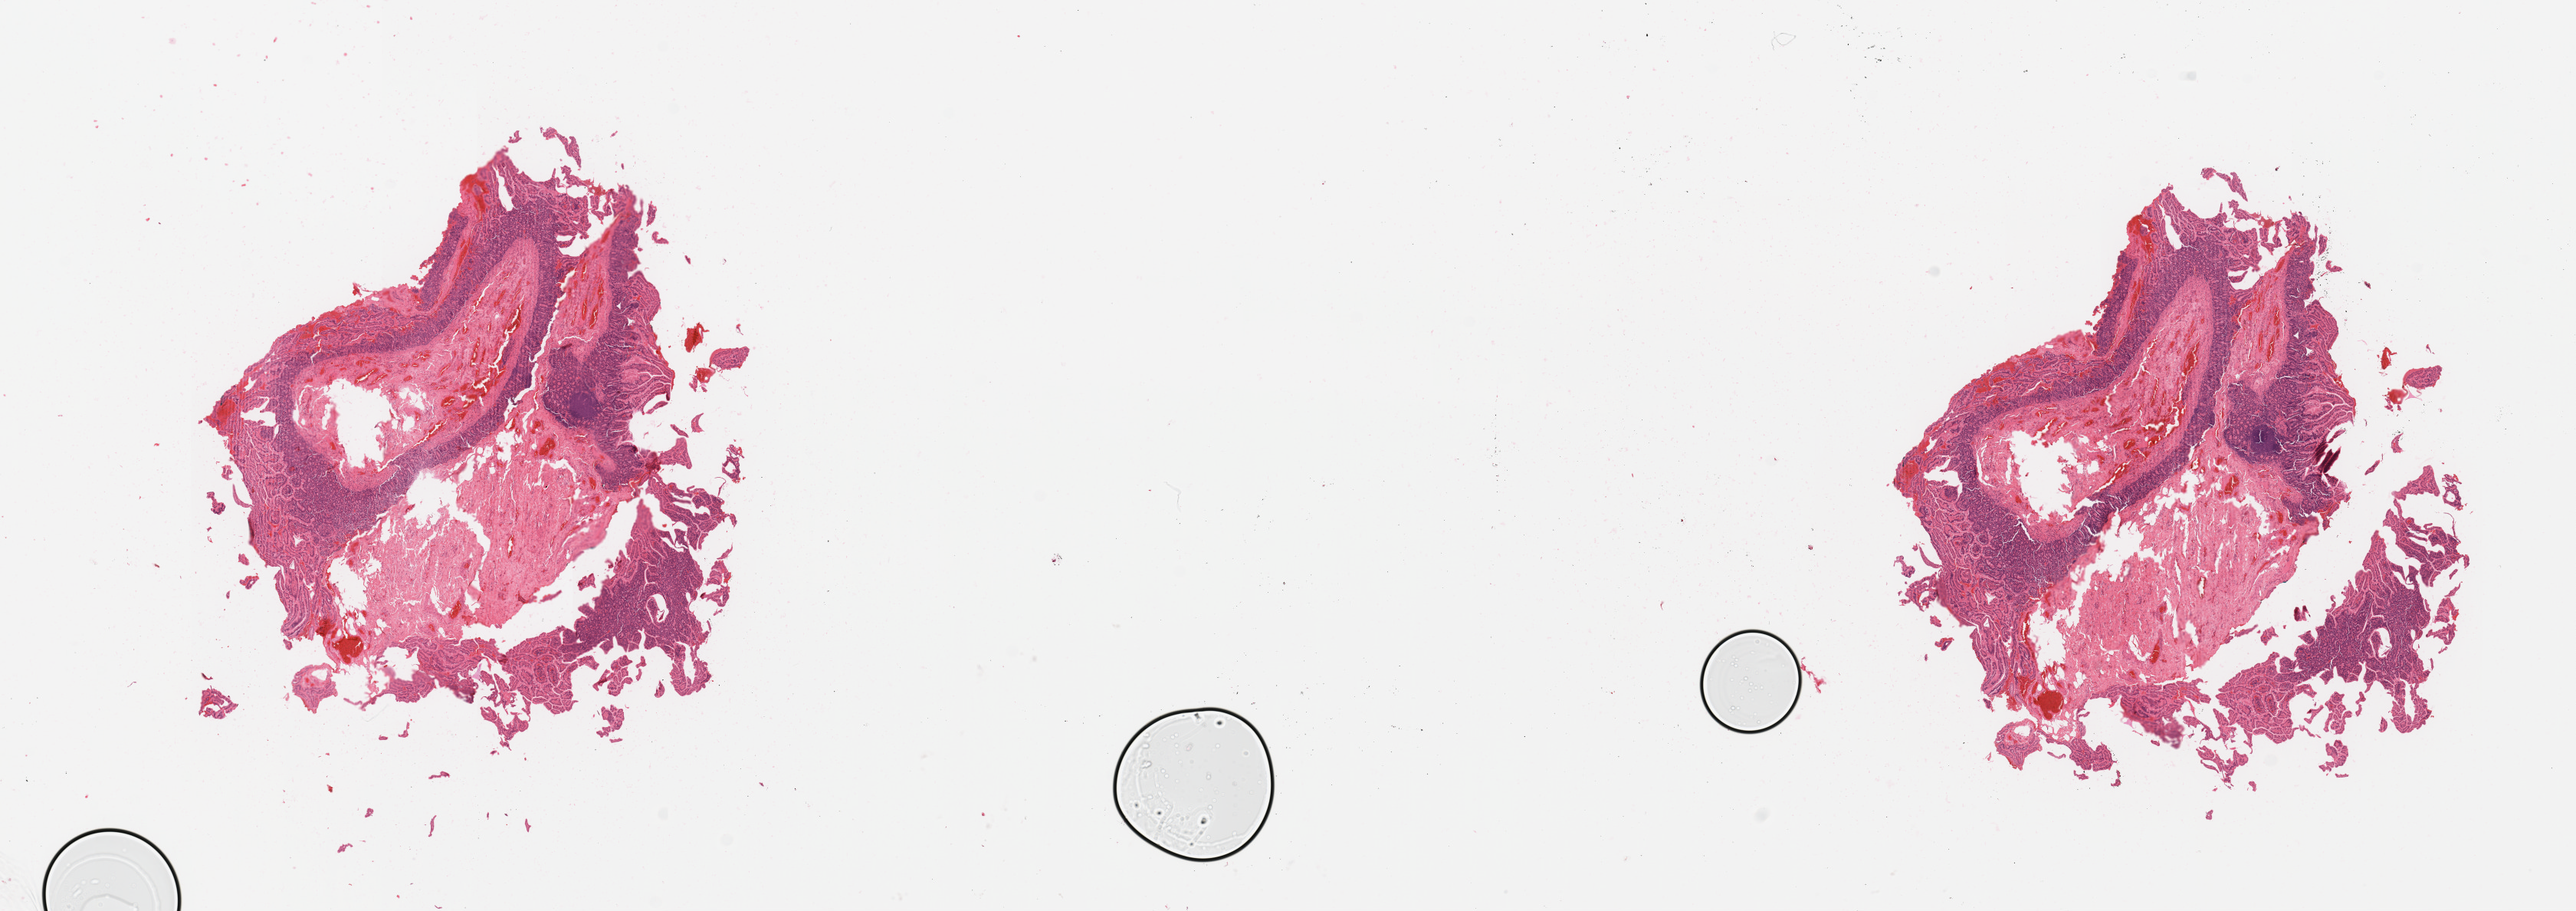
Whole-slide histology image, Hematoxylin and eosin (H&E) stained — whole scanned area (about 26.6 x 9.4 mm) shown as a low-resolution overview, normal (non-tumour) tissue sample, sampled site: pancreas. Patient: male, age 64 years.
This section: normal (non-tumour) tissue from the same patient. Patient diagnosis: Infiltrating duct carcinoma, NOS.